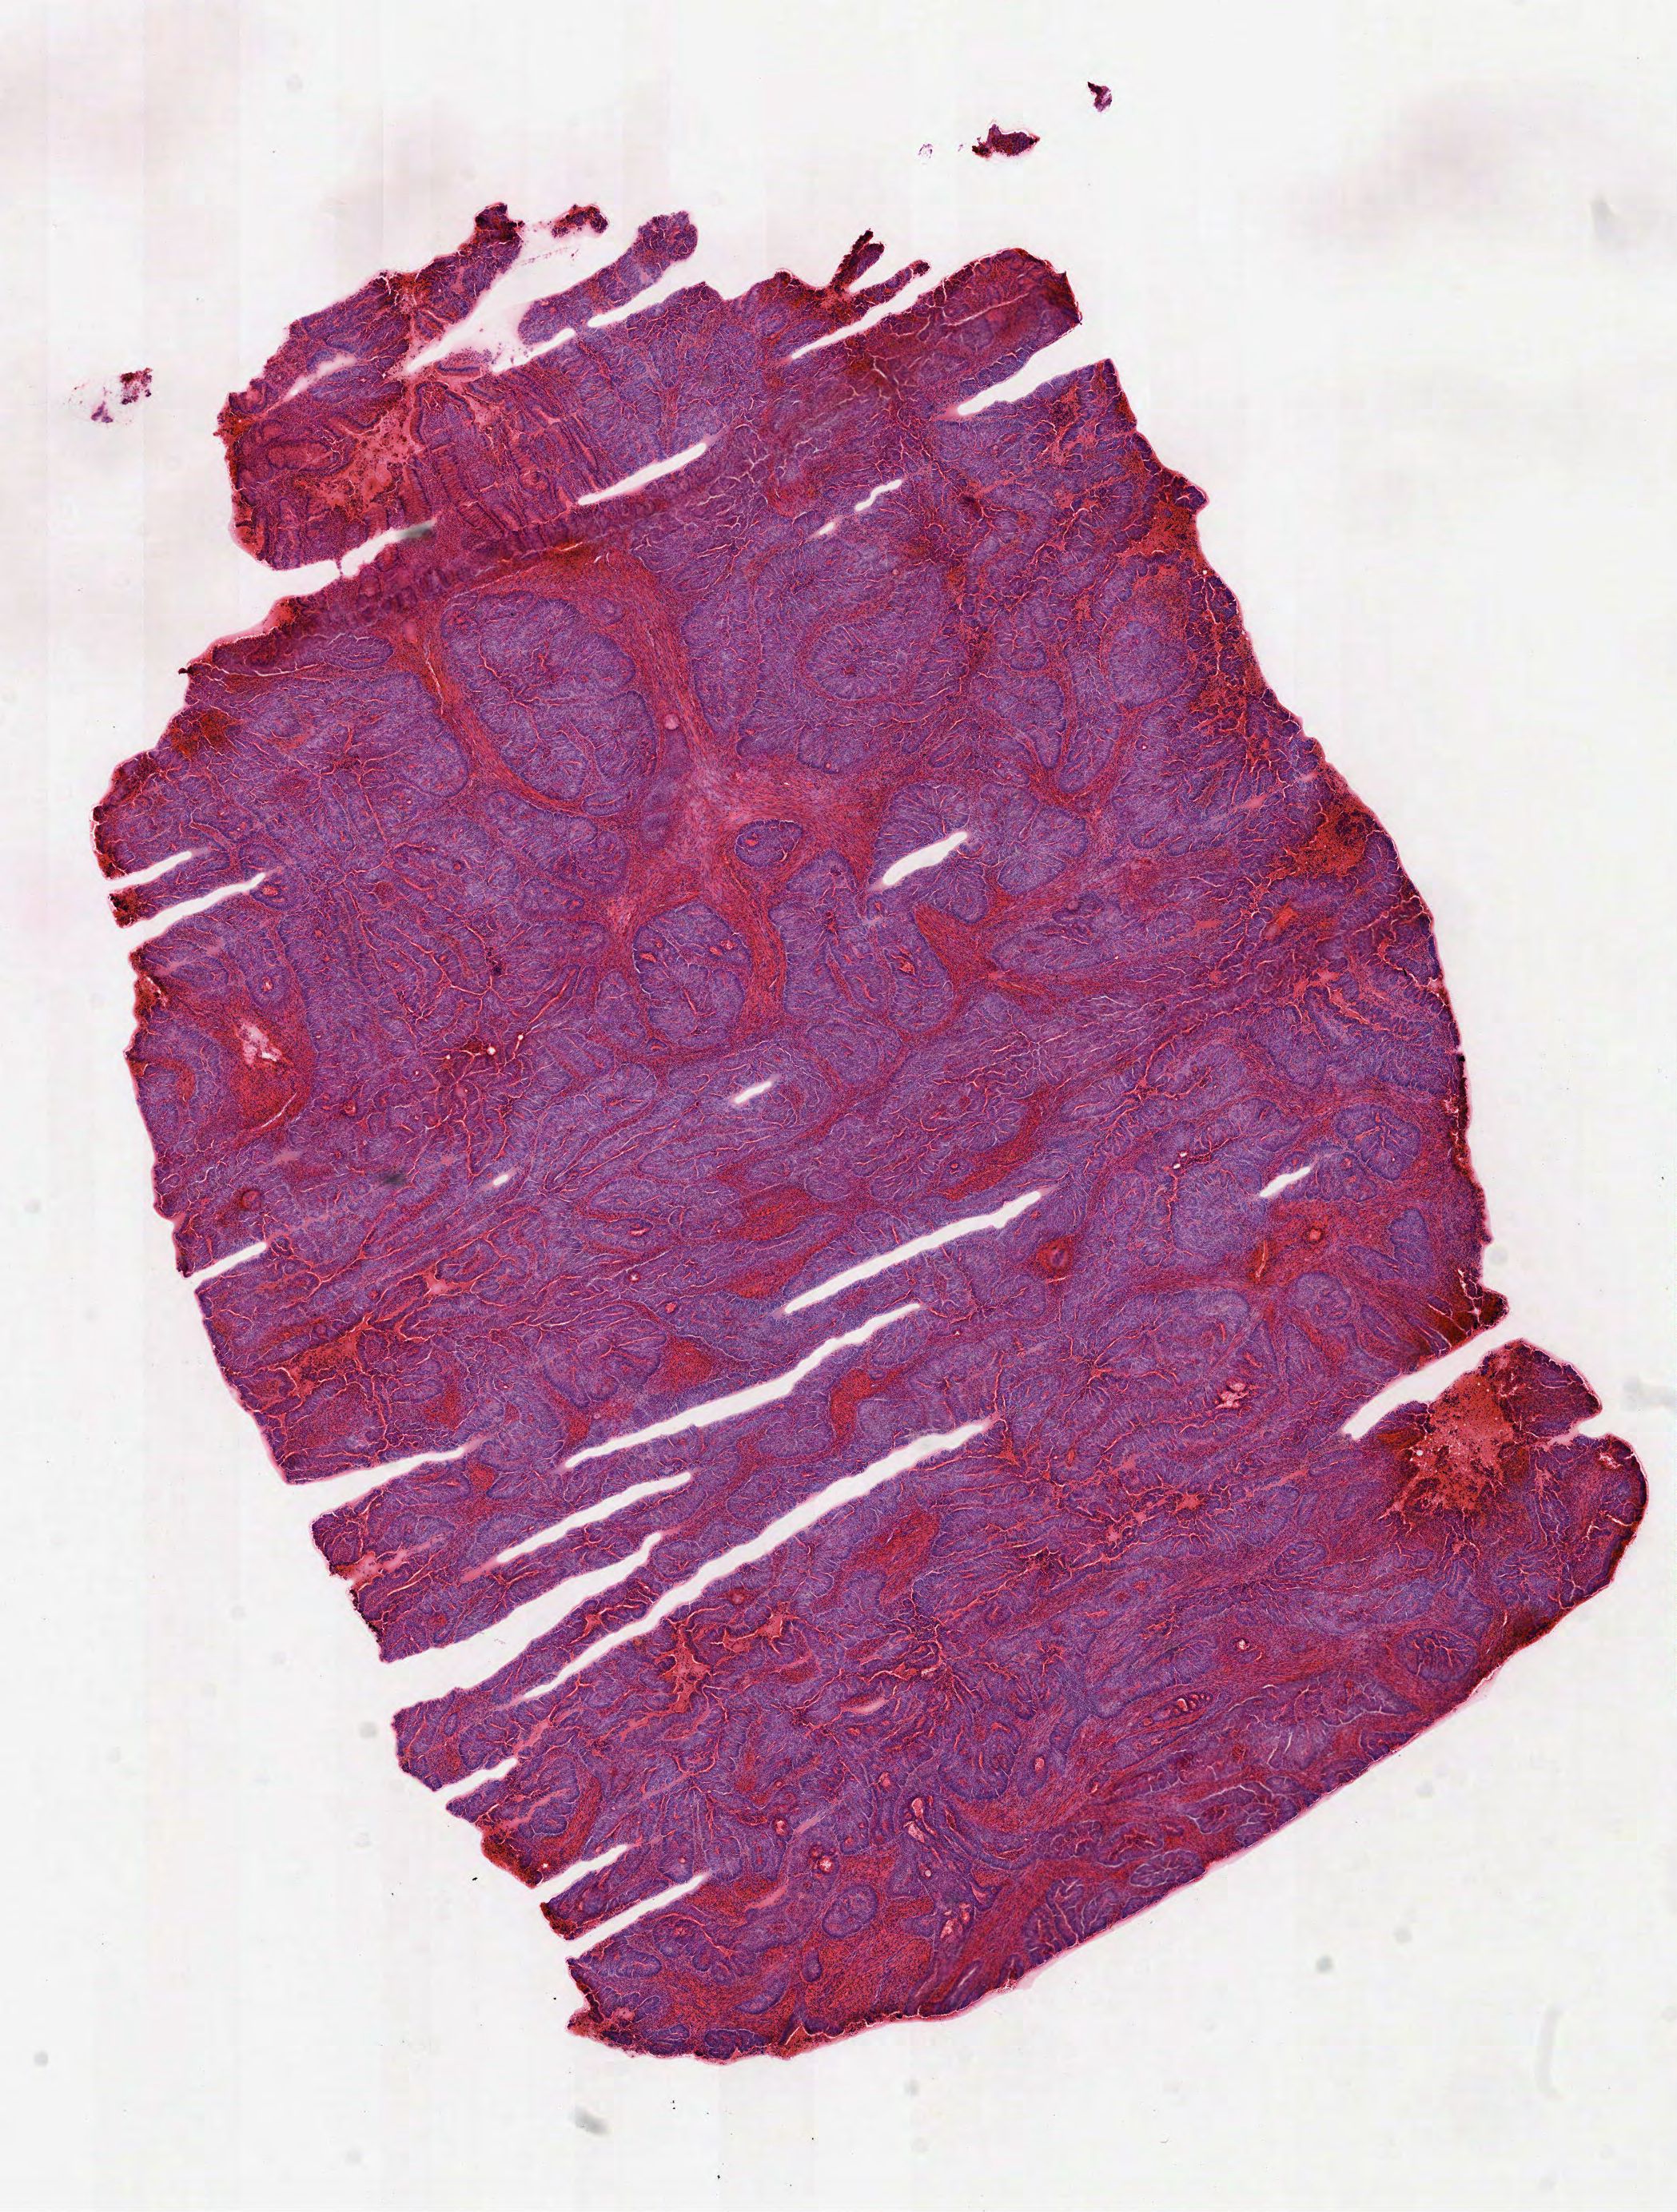
Whole-slide histology image, H&E-stained — low-resolution overview of the scanned area, about 8.5 x 11.2 mm (acquisition: 40x scan); frozen section from the top of the tissue portion; primary tumour sample from the rectum. Patient: female, age at initial diagnosis 48 years. Pathologist review of this section (percent, as recorded): tumour cells 74%, tumour nuclei 75%.
Diagnosis: Adenocarcinoma in tubulovillous adenoma.